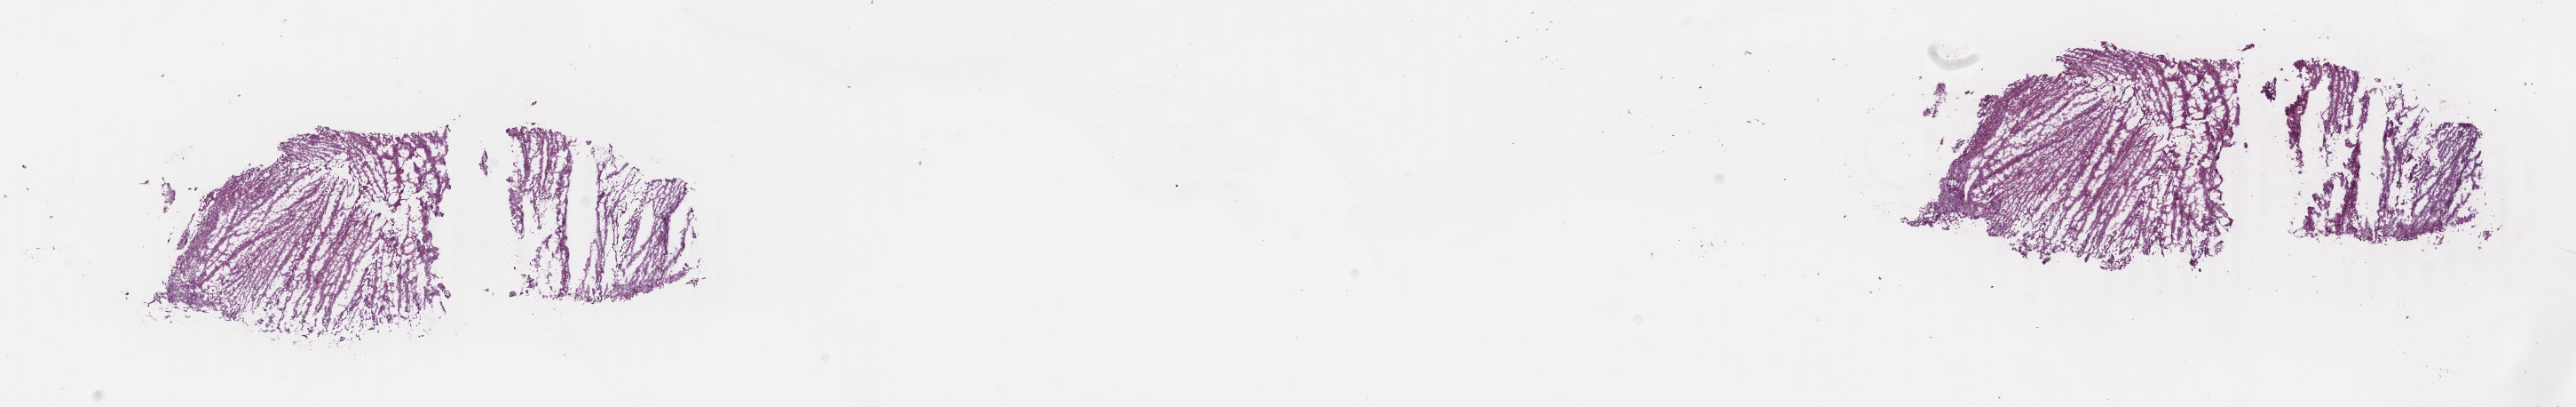
Whole-slide histology image, H&E, whole scanned area (about 23.1 x 3.6 mm, from a 40x scan) shown as a low-resolution overview; frozen section from the top of the tissue portion; sample: primary tumour, brain. Patient: male, age at initial diagnosis 27 years. Histologic grade: G2 (moderately differentiated). Pathologist review of this section (percent, as recorded): tumour cells 30%, tumour nuclei 80%, normal cells 20%, stromal cells 50%, necrosis 0%. Infiltration values recorded for this section: lymphocyte infiltration 0%, monocyte infiltration 5%, neutrophil infiltration 0%.
Laterality: right. Diagnosis: Oligodendroglioma, NOS.